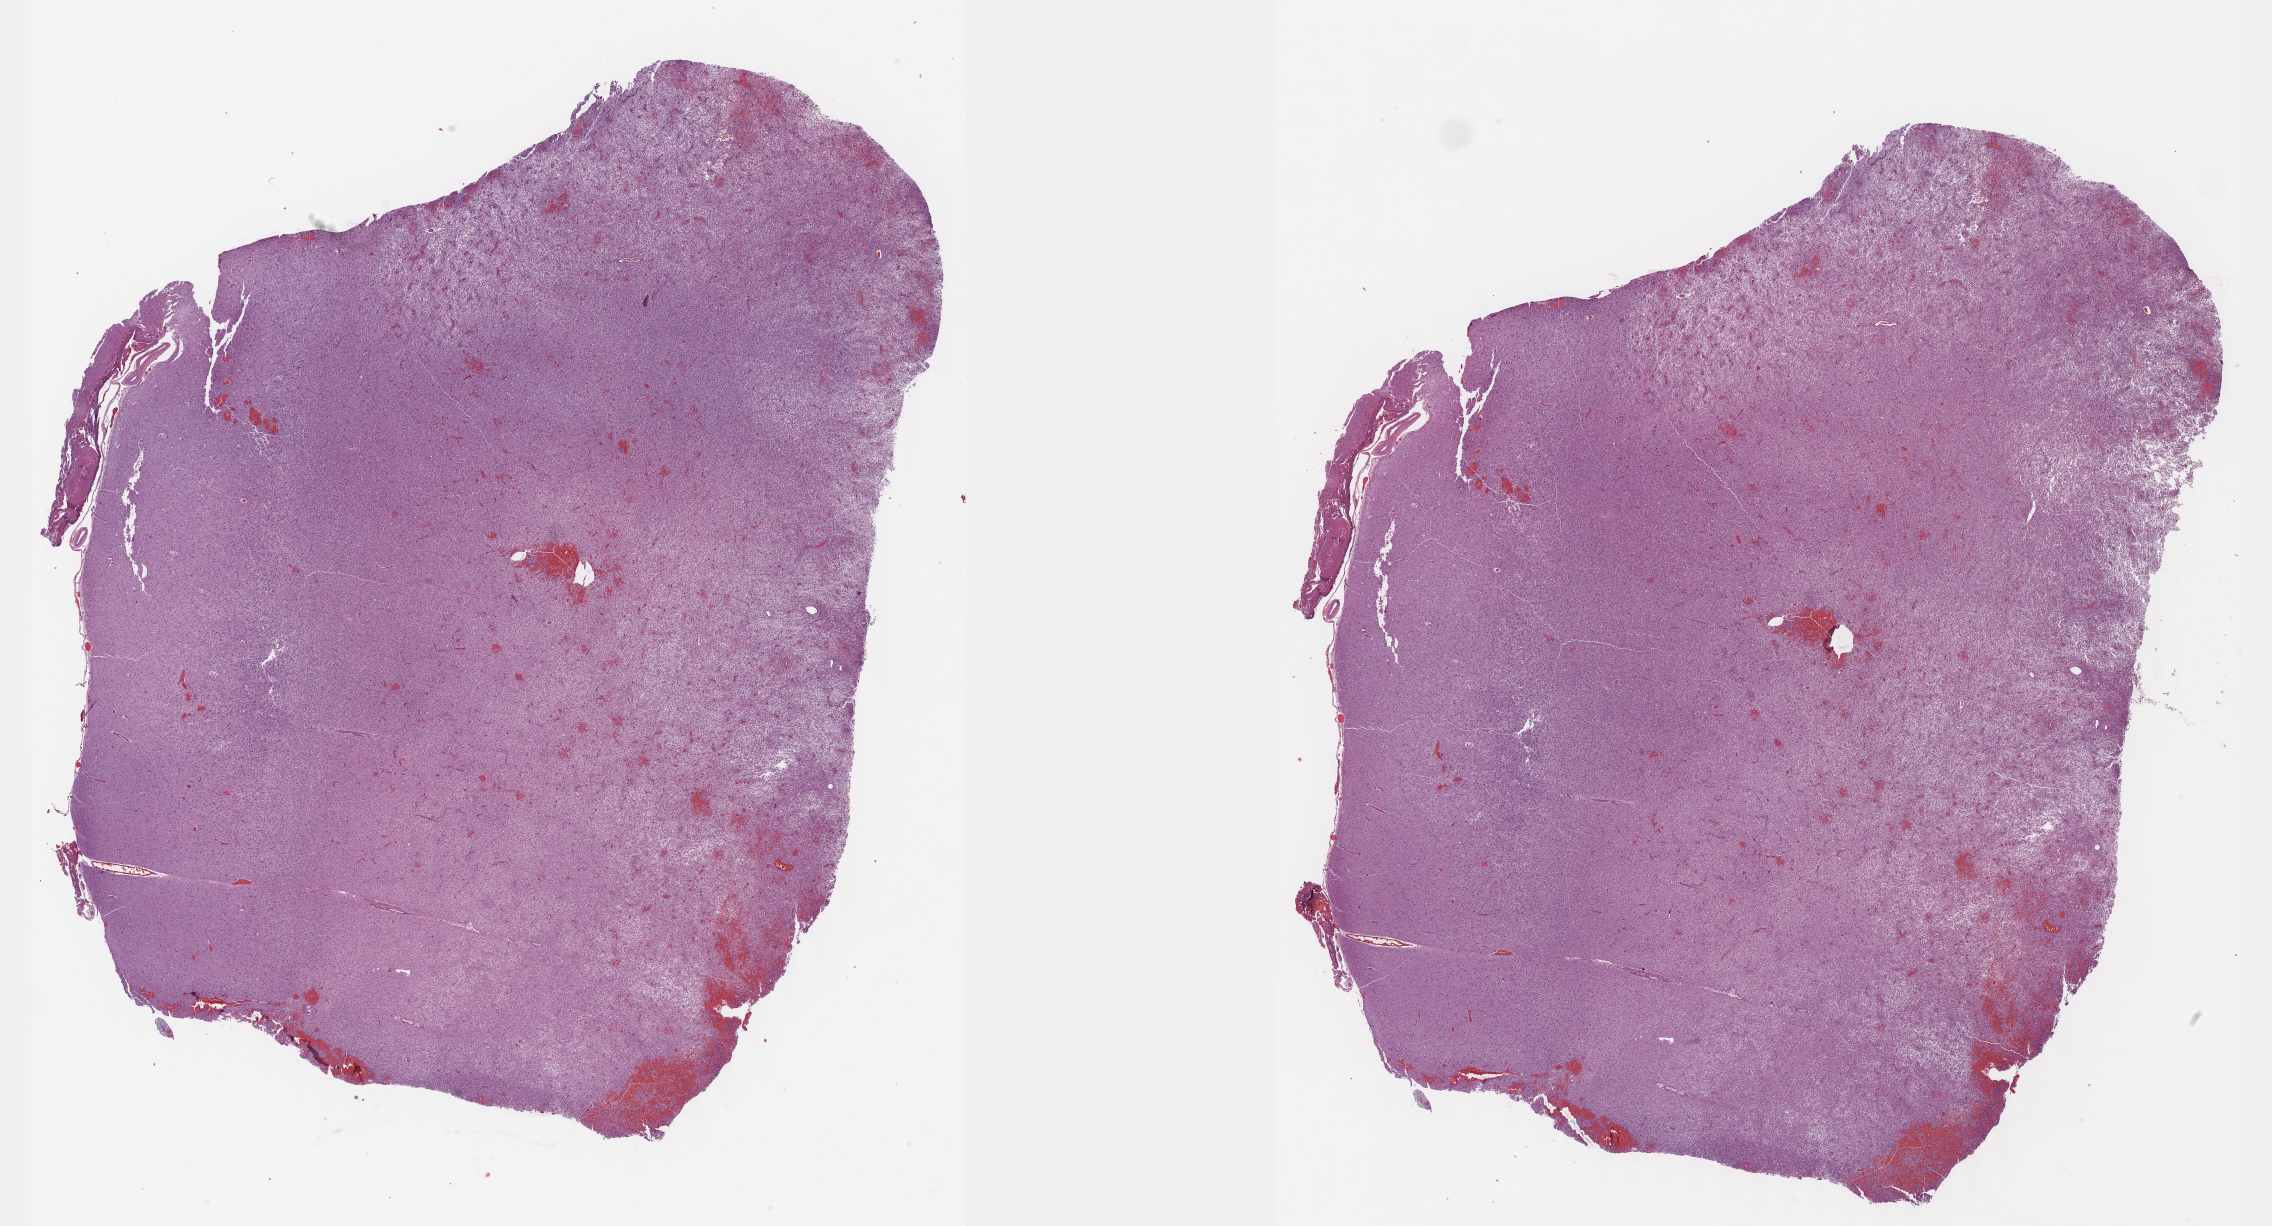
Digitized H&E tissue section (whole slide), low-resolution overview of the scanned area, about 36.7 x 19.8 mm; formalin-fixed paraffin-embedded (FFPE) diagnostic section; sample: primary tumour, brain. Female patient; age at initial diagnosis 52 years. Histologic grade: G3 (poorly differentiated).
Diagnosis: Astrocytoma, anaplastic (cerebrum).